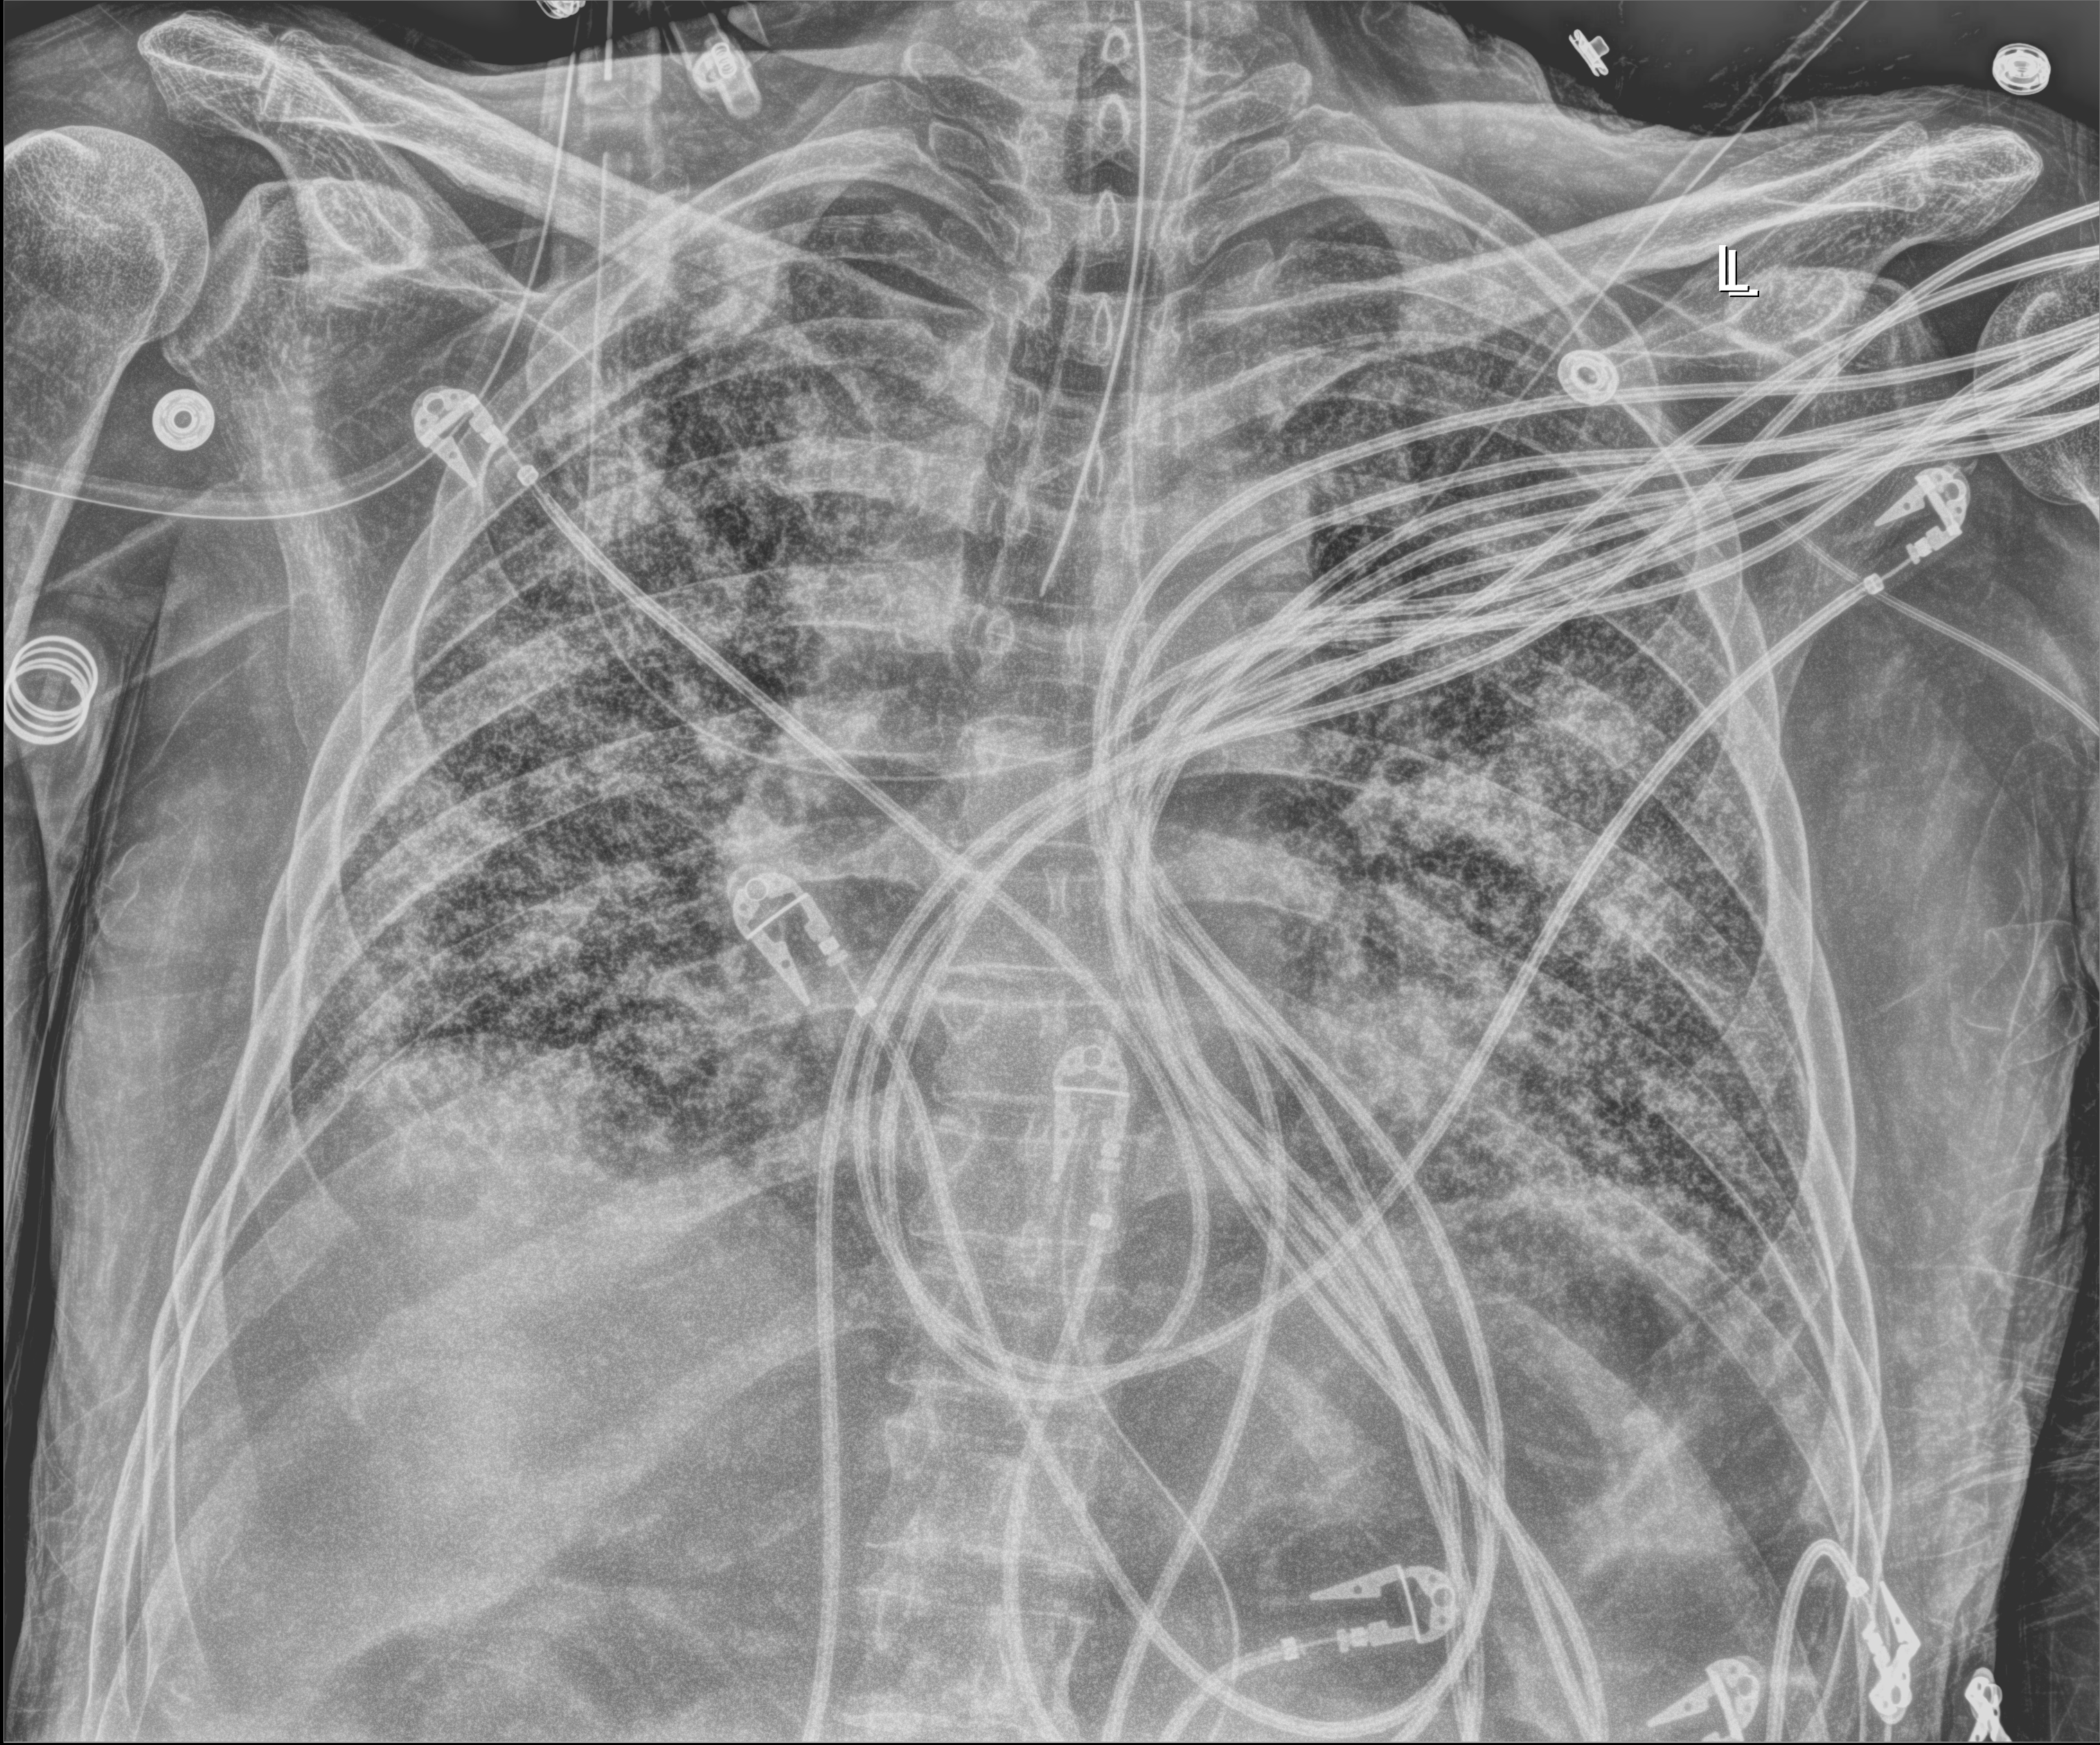
Portable chest radiograph; anteroposterior (AP) projection. Patient hospitalised with COVID-19; male, aged 60–74 years.
Hospital-stay facts (about this admission, not read from this image; timing relative to this image not recorded): mechanically ventilated during this hospital stay: yes; admitted to intensive care during this hospital stay: yes.